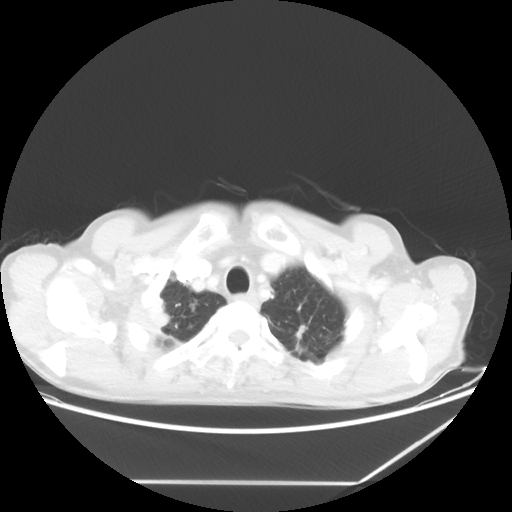
Chest CT, one axial slice; position 58 of 65 along the scan axis; lung window (W 1500 / L -600 HU); 512 × 512 image matrix. Patient: male, 68 years. From the clinical record (not read from this slice): clinical TNM (as recorded): T3 N3 M0.
Structures marked on this image (rectangle marked by the reading radiologist):
- lung tumour (recorded histology: adenocarcinoma): bounding box (x1, y1, x2, y2) in pixels: (139, 288, 178, 342)